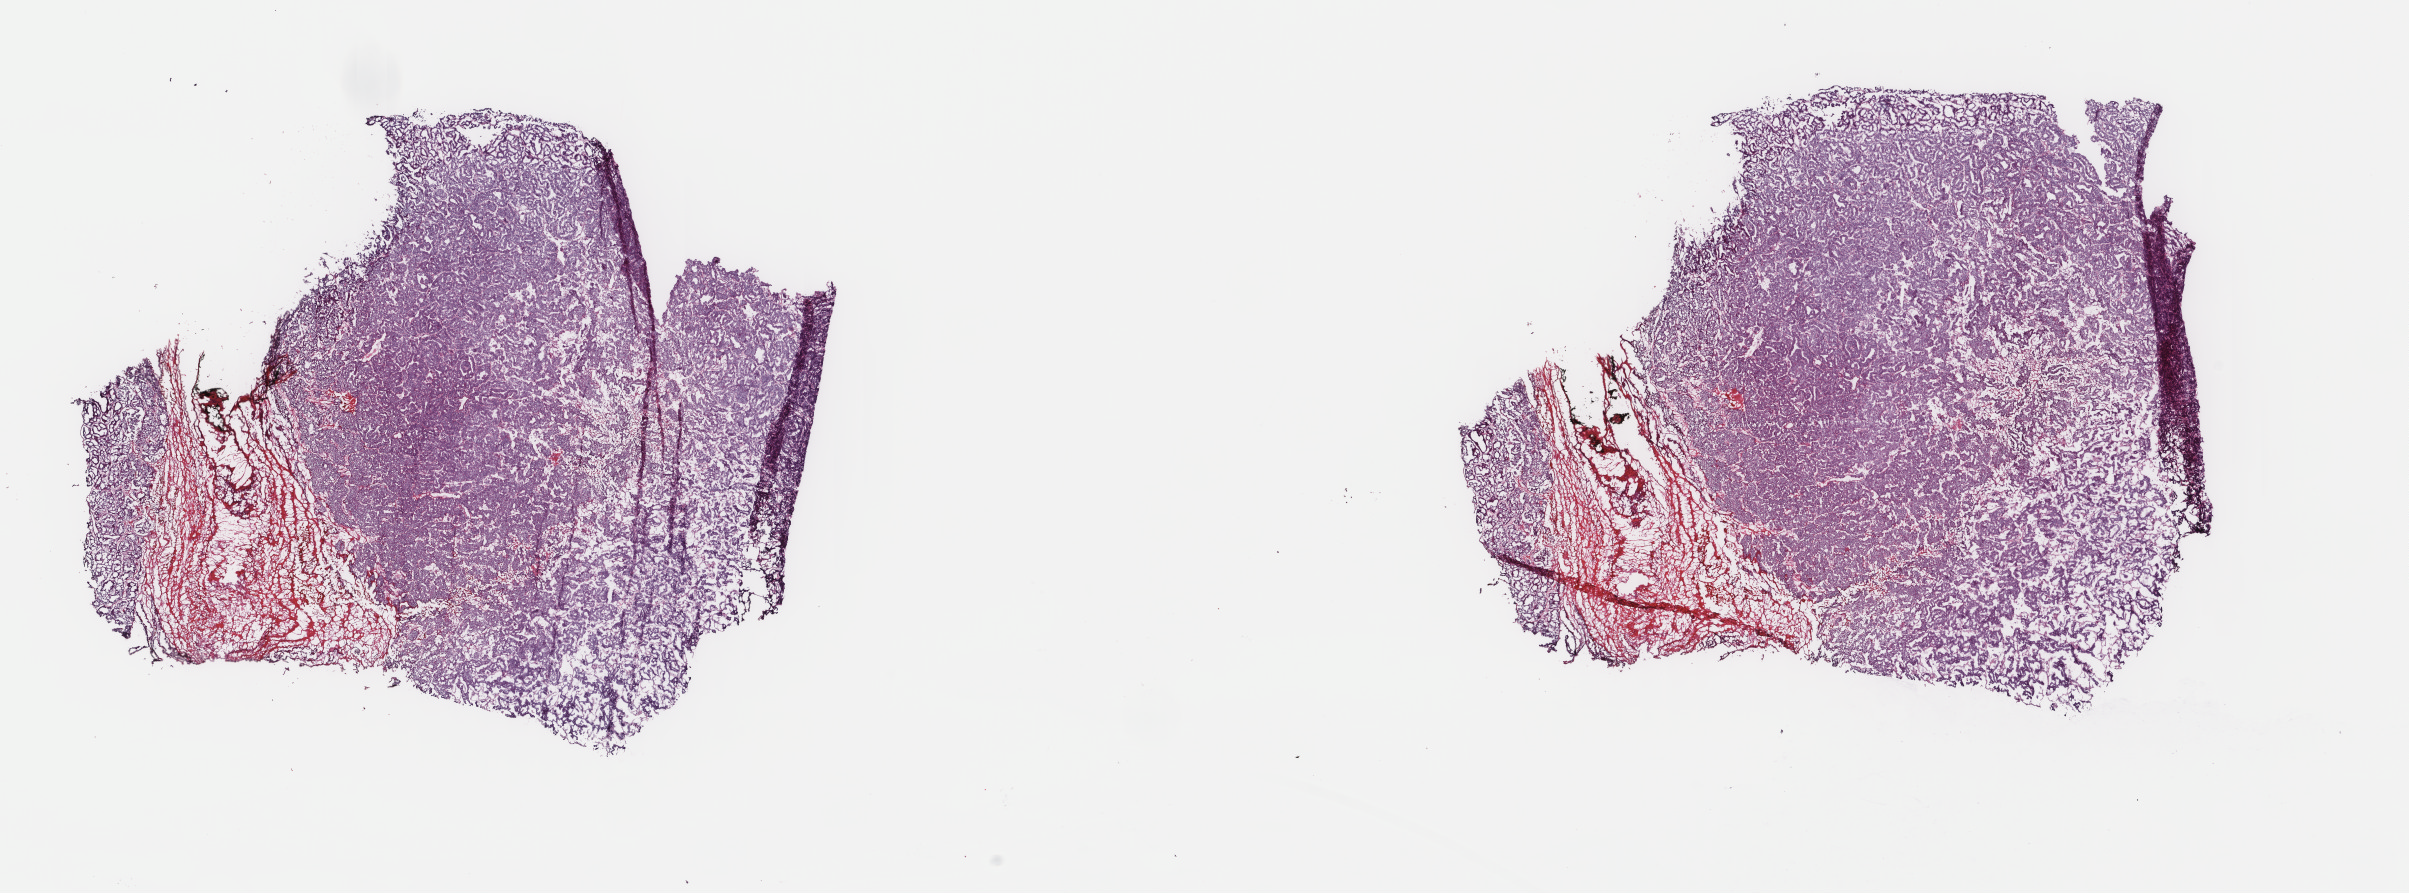
Whole-slide histology image, H&E — whole scanned area (about 19.1 x 7.1 mm) shown as a low-resolution overview; frozen section from the top of the tissue portion; thyroid, primary tumour sample. Female, age 30 years at initial diagnosis. Pathologist review of this section (percent, as recorded): tumour cells 85%, tumour nuclei 85%, normal cells 0%, stromal cells 15%, necrosis 0%. Infiltration values recorded for this section: lymphocyte infiltration 2%, monocyte infiltration 1%, neutrophil infiltration 0%.
TNM: T2 NX MX. Laterality: left. Pathologic diagnosis: Papillary adenocarcinoma, NOS (thyroid gland). AJCC pathologic stage: I (7th edition).